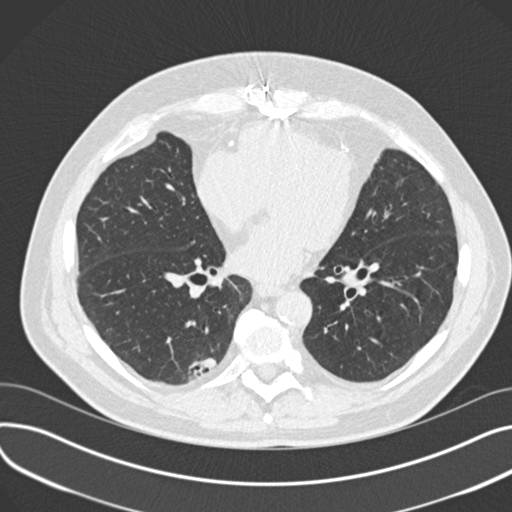
Low-dose screening chest CT, axial slice; third annual screen; lung window (W 1500 / L -600 HU); 2 mm slice thickness; 512 × 512 image matrix, field of view 372 × 372 mm. Male, age 68 years at enrolment. Former smoker at enrolment.
Lesion marked by an expert reader, bounding box (x1, y1, x2, y2) in pixels: (177, 347, 221, 387). The screening reader recorded 4 non-calcified nodules or masses ≥4 mm on this exam (left upper lobe, lingula, right upper lobe, right lower lobe); which of them this box marks is not recorded.